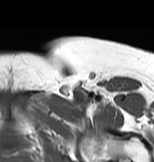
MRI of an extremity soft-tissue mass, one axial slice. Position 58 of 83 along the scan axis. MR volume resampled by the dataset authors to the PET/CT grid (not the native acquisition matrix). 154 × 162 image matrix, field of view 150 × 158 mm. Female patient. From the clinical record (not read from this slice): histological type: myxofibrosarcoma; grade: intermediate; site of the primary tumour: left thigh.
Annotated regions visible in this slice (expert contour drawn on MRI and transferred to this co-registered scan by the dataset authors):
- gross tumour volume including surrounding oedema: bounding box (x1, y1, x2, y2) in pixels: (49, 91, 114, 113)